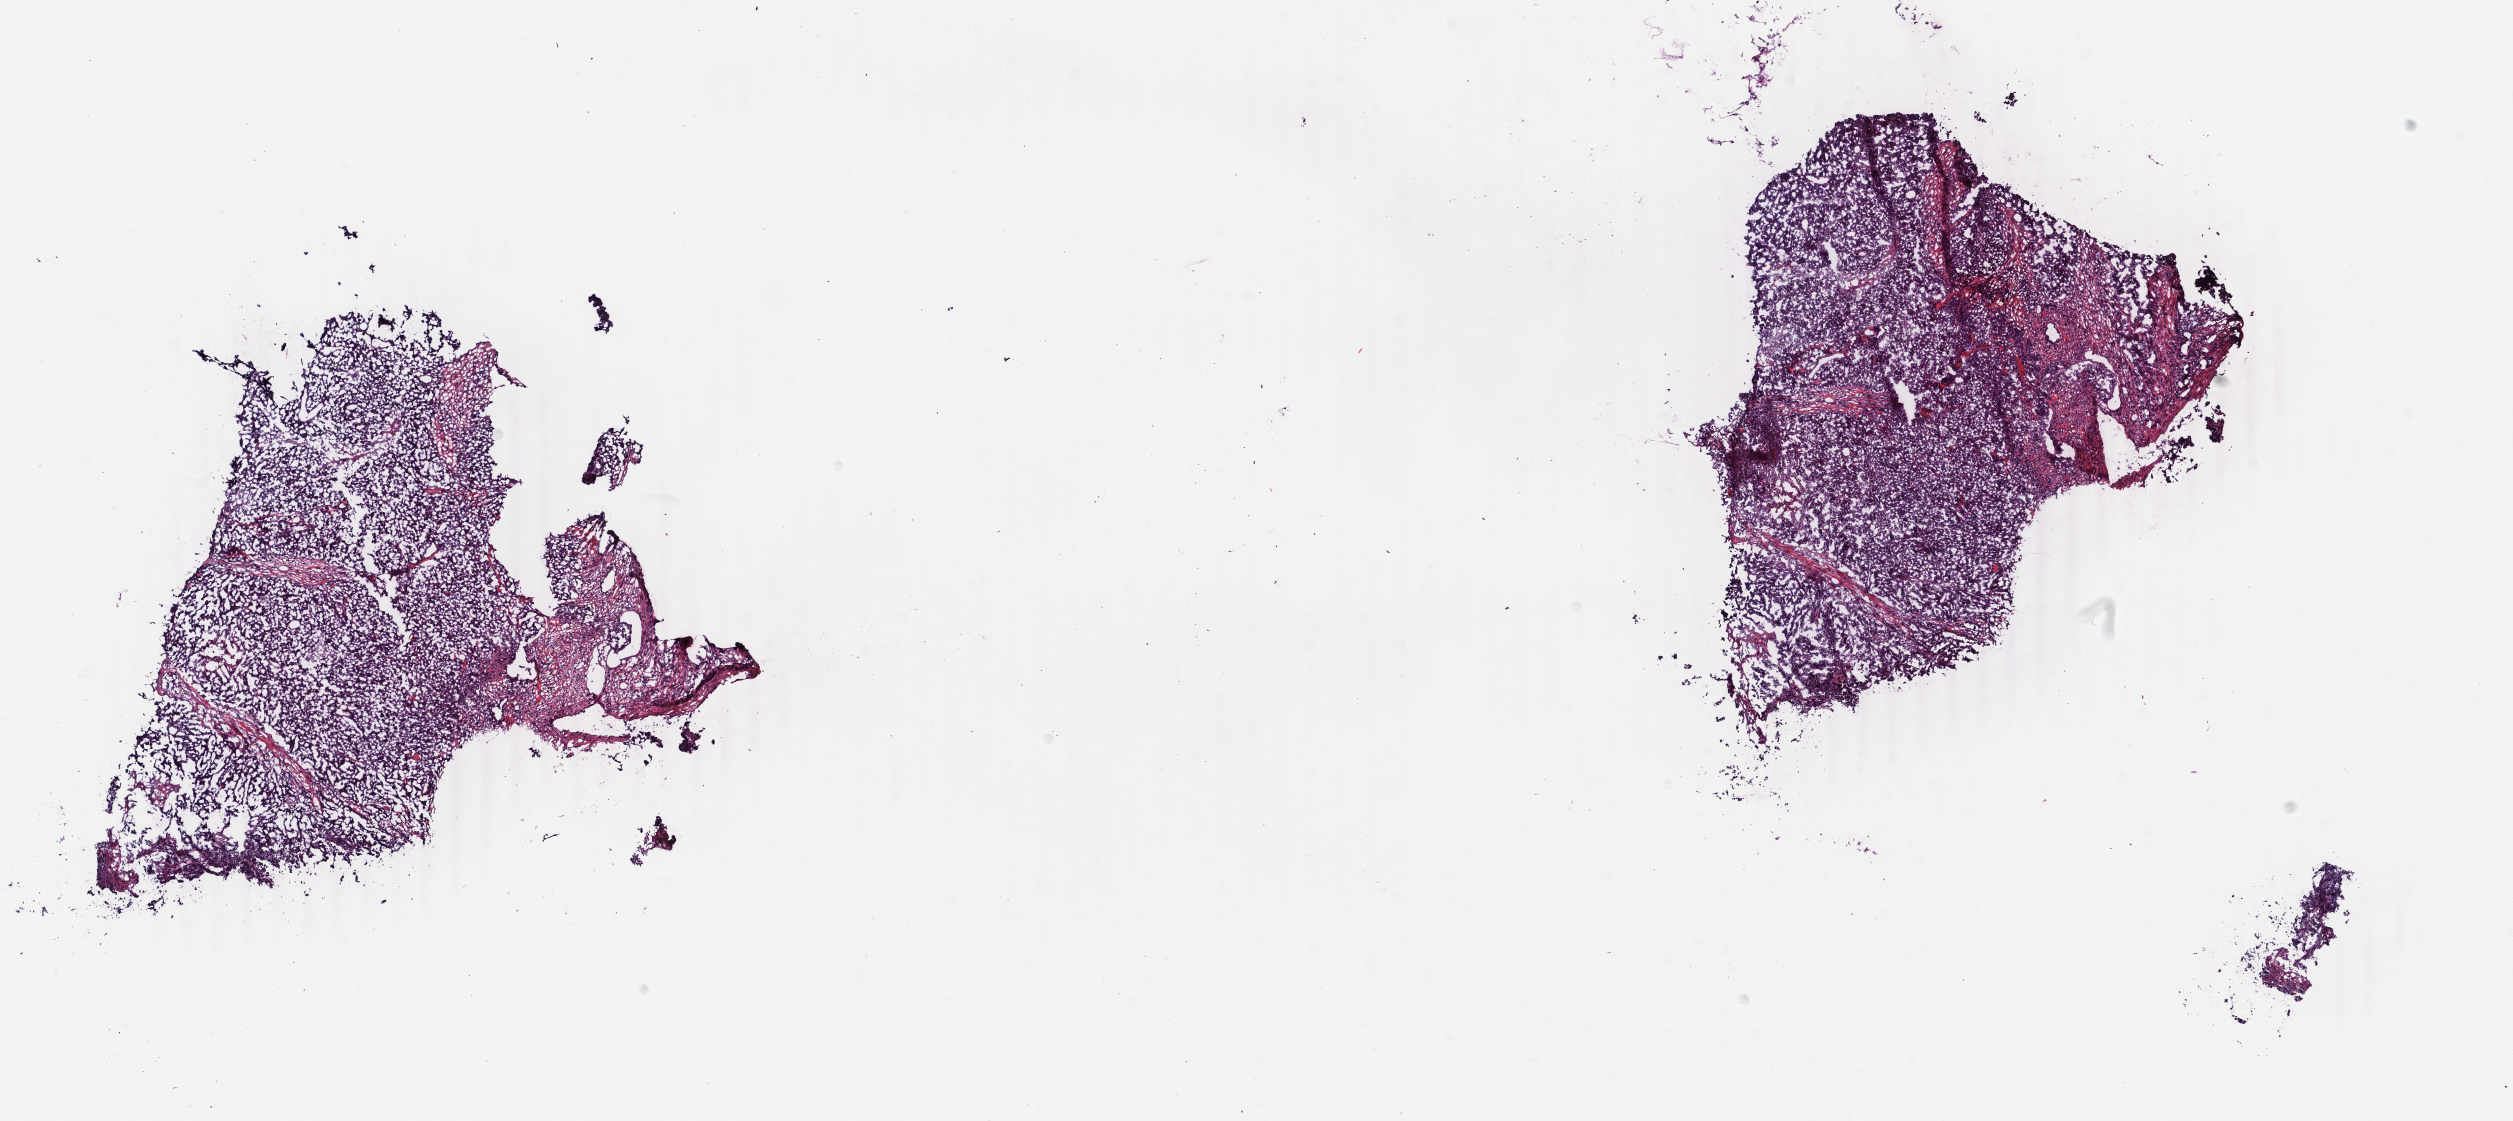
Whole-slide histology image, H&E, a low-resolution overview of the entire scanned area, about 20.0 x 8.9 mm (slide scanned at 40x); frozen section from the top of the tissue portion; sample: primary tumour, breast. Patient: female, age at initial diagnosis 45 years. Slide review estimates, as recorded: tumour cells 90%, tumour nuclei 90%, normal cells 0%, stromal cells 10%, necrosis 0%. Inflammatory infiltration, as recorded: lymphocyte infiltration 1%, monocyte infiltration 0%, neutrophil infiltration 0%.
AJCC pathologic stage: IA. Laterality: left. Lymph nodes positive (case pathology): 0 of 8 examined. Diagnosis: Infiltrating duct carcinoma, NOS.